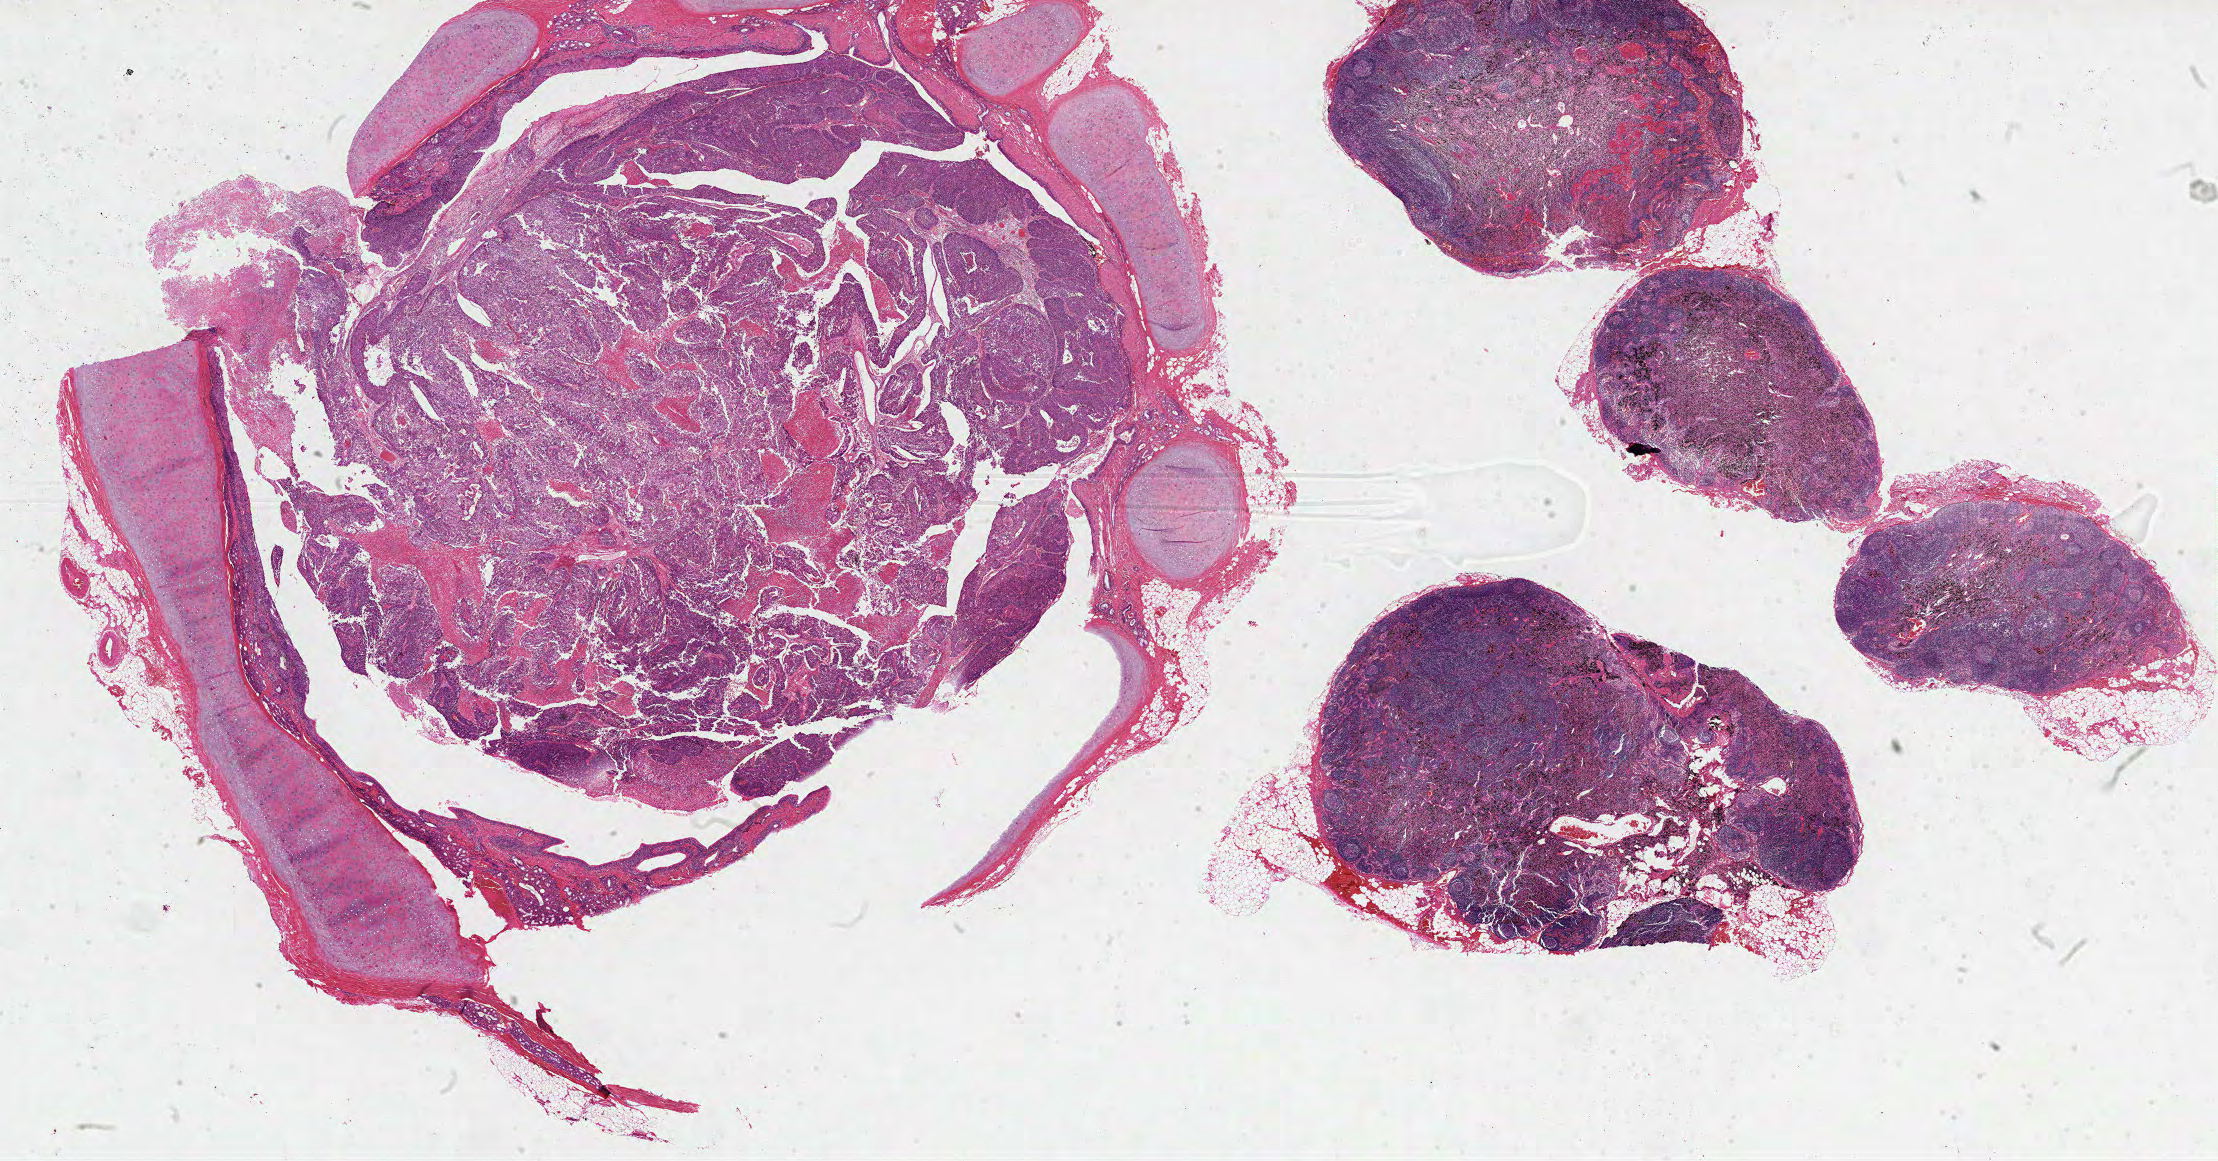
Whole-slide histology image, Hematoxylin and eosin (H&E) stained — a low-resolution overview of the entire scanned area, about 35.8 x 18.7 mm; formalin-fixed paraffin-embedded (FFPE) diagnostic section; sample: primary tumour, lung. Male patient; age at initial diagnosis 64 years.
Laterality: left. Histologic diagnosis: Squamous cell carcinoma, NOS (upper lobe, lung). AJCC pathologic stage: IB (6th edition).